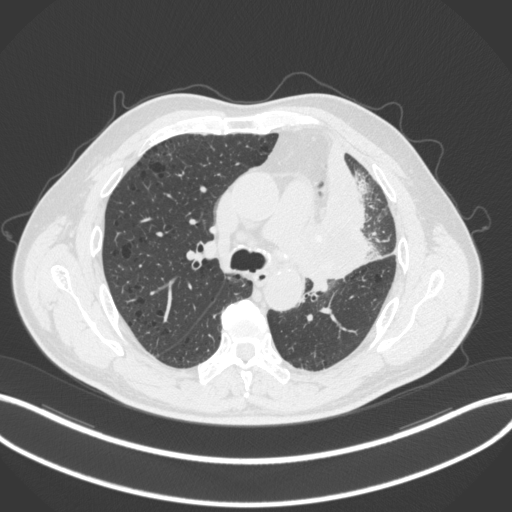
Chest CT, one axial slice; slice 184 of 286 in the series (ordered by position); lung window (W 1500 / L -600 HU); 1 mm slice thickness; 512 × 512 image matrix, field of view 400 × 400 mm. Male patient, age 68 years. From the clinical record (not read from this slice): clinical TNM (as recorded): T3 N3 M1.
Annotated regions visible in this slice (bounding box drawn by a radiologist):
- lung tumour (recorded histology: adenocarcinoma): bounding box [x1, y1, x2, y2] px = [311, 187, 382, 278]